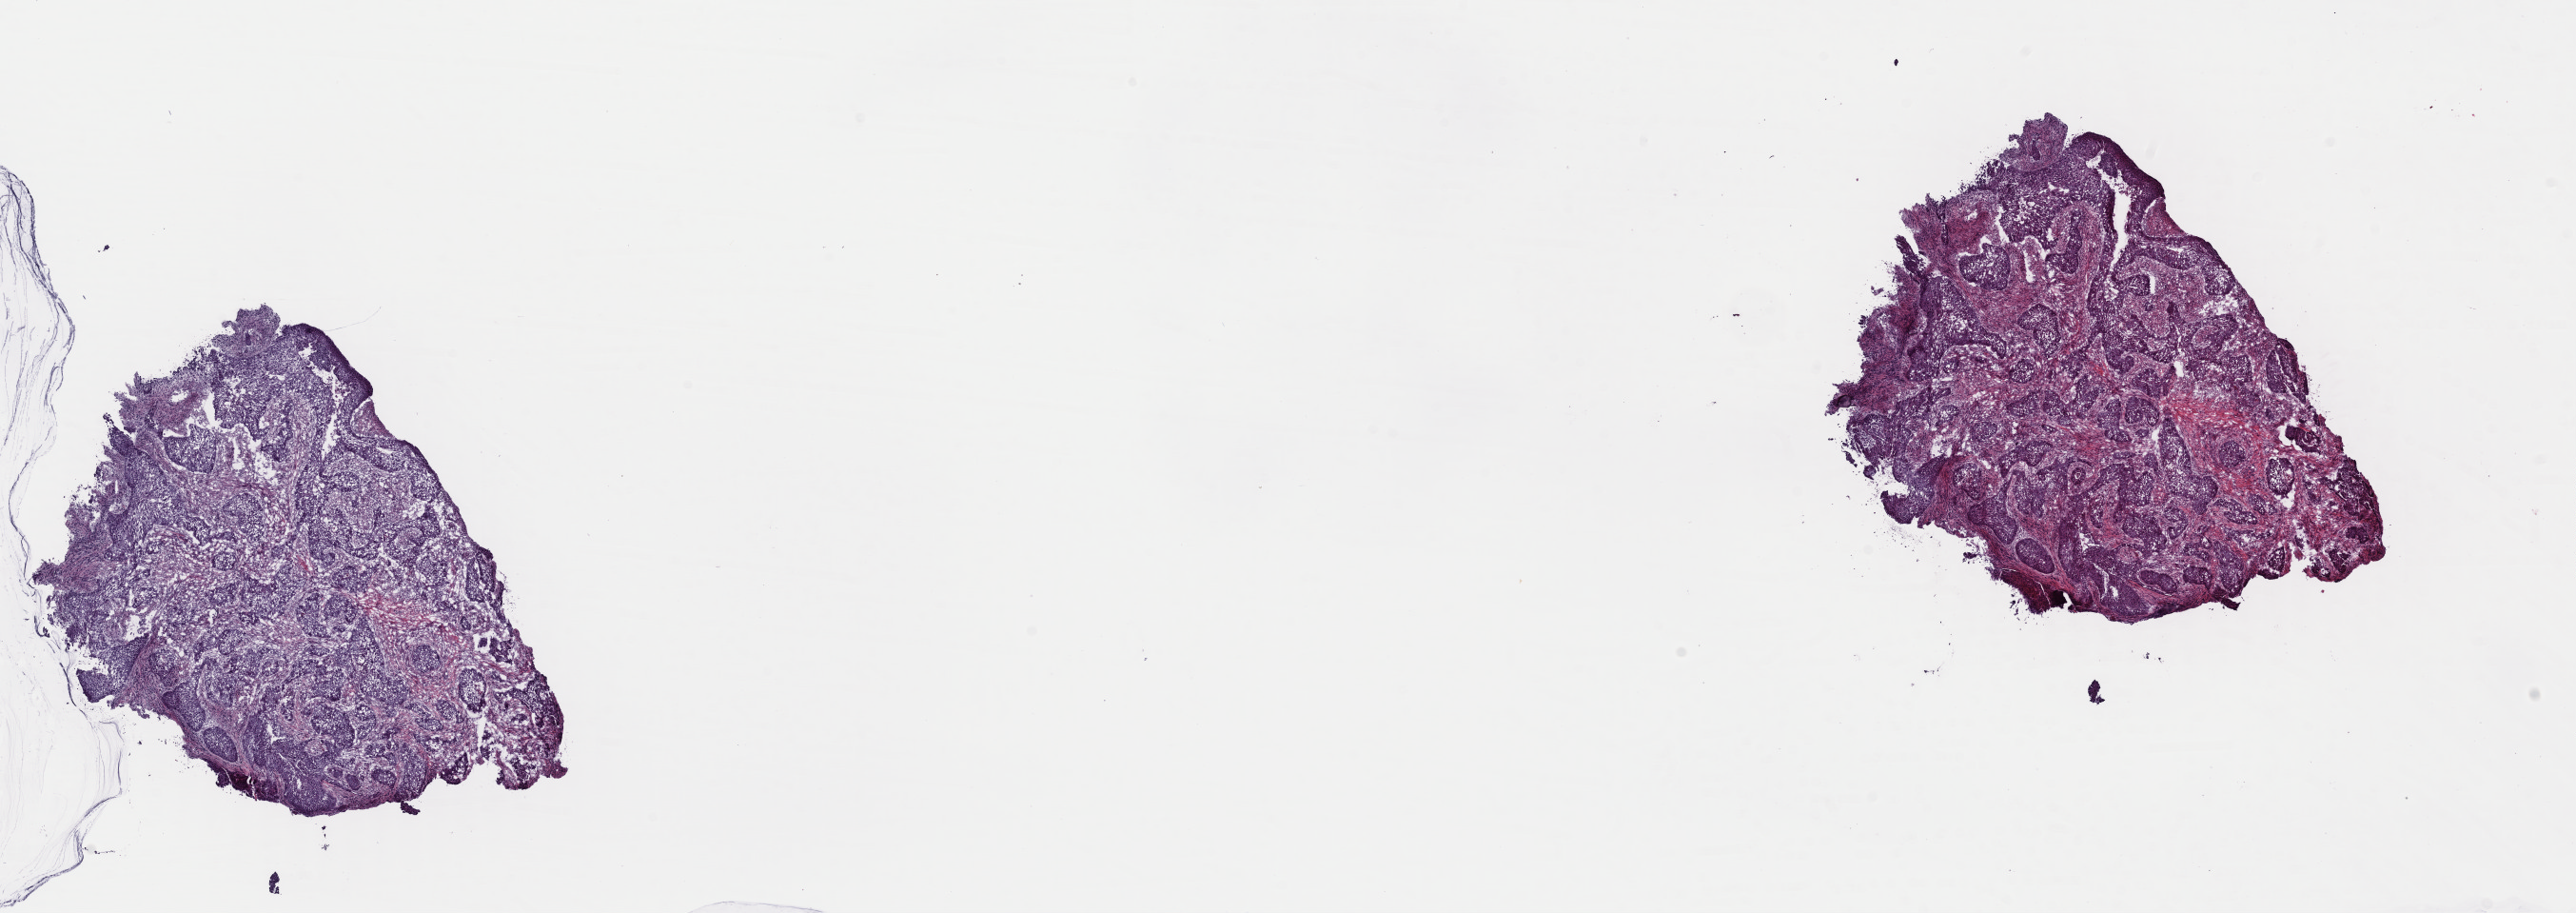
H&E whole-slide image, shown as a low-resolution overview of the whole scanned area (about 21.4 x 7.6 mm); frozen section; sample: primary tumour, lung. Male patient; age at initial diagnosis 81 years. Slide review estimates, as recorded: tumour cells 50%, tumour nuclei 70%, normal cells 0%, stromal cells 45%, necrosis 5%. Inflammatory infiltration, as recorded: lymphocyte infiltration 0%, monocyte infiltration 0%, neutrophil infiltration 0%.
• AJCC pathologic stage: IA
• histologic diagnosis: Squamous cell carcinoma, NOS